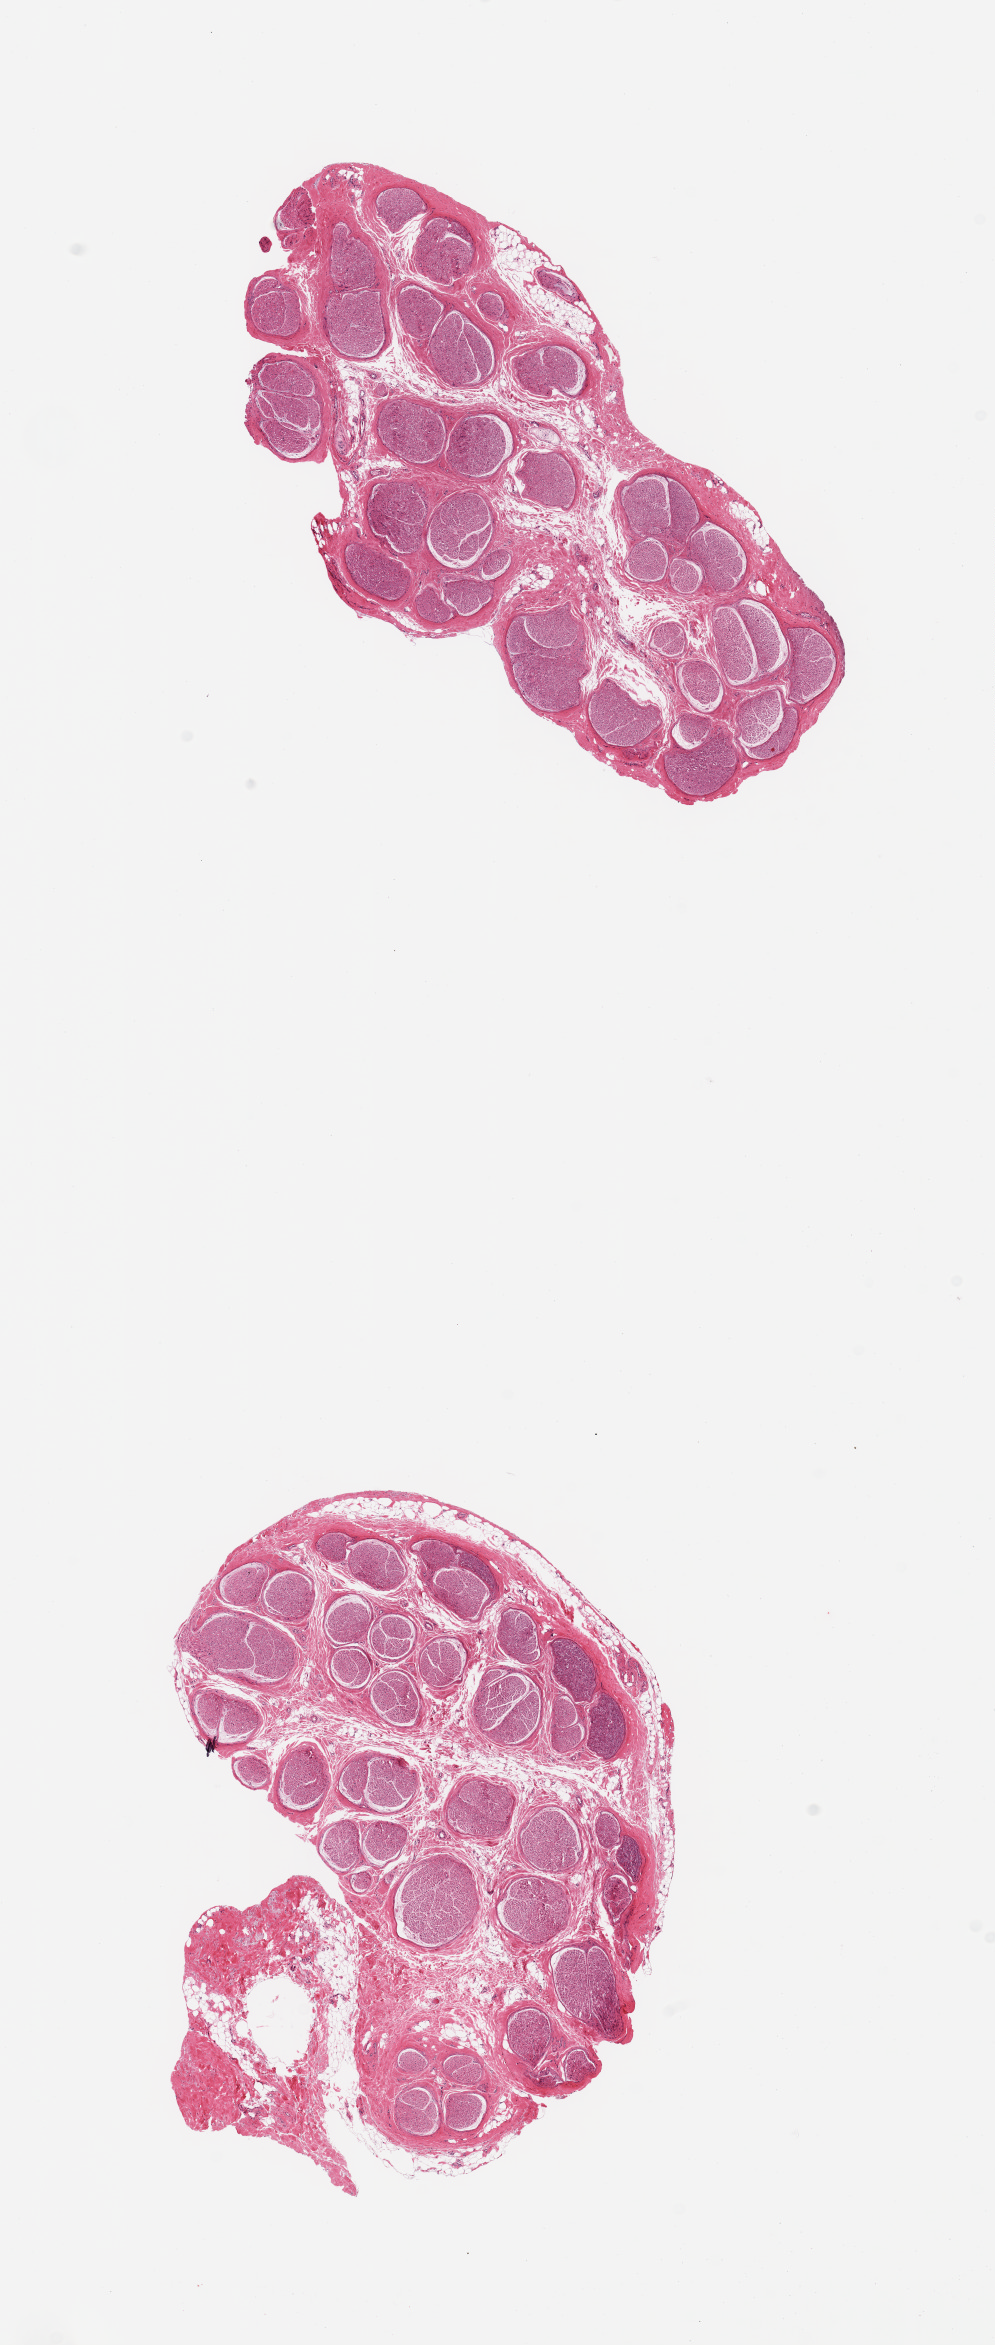
Hematoxylin and eosin (H&E) whole-slide image, brightfield — a low-resolution overview of the entire scanned area, about 7.9 x 18.6 mm. PAXgene-fixed, paraffin-embedded tissue. Section of tibial nerve (target tissue). Tissue donor sample. Female donor.
Reviewer comment on this tissue sample: 2 pieces; ~5-10% internal fat, 1 piece has 10% attachment of fat/fibrous tissue.